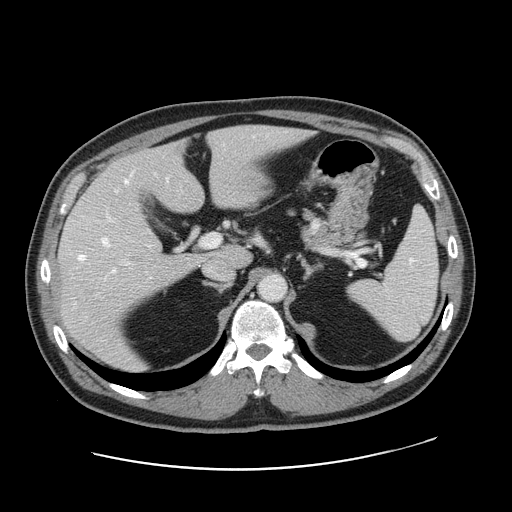
Contrast-enhanced abdominal CT, one axial slice; slice 102 of 178 in the series (ordered by position); 120 kVp; intravenous contrast given; soft-tissue window (W 400 / L 40 HU); 2.5 mm slice thickness; 512 × 512 image matrix, field of view 403 × 403 mm. Male patient, age 63 years. Case-level facts recorded for this patient, not image findings: diagnosis: colorectal cancer liver metastases, imaged before liver resection; multiple liver metastases: yes.
Outlined on this slice (manually delineated by an expert):
- hepatic veins: box from (x=79, y=180) to (x=128, y=270) px
- liver: (x=60, y=126)–(x=302, y=370)
- planned liver remnant (the part of the liver to remain after resection): (x=121, y=126)–(x=304, y=265)
- portal vein (with intrahepatic branches): (x=124, y=234)–(x=221, y=264)